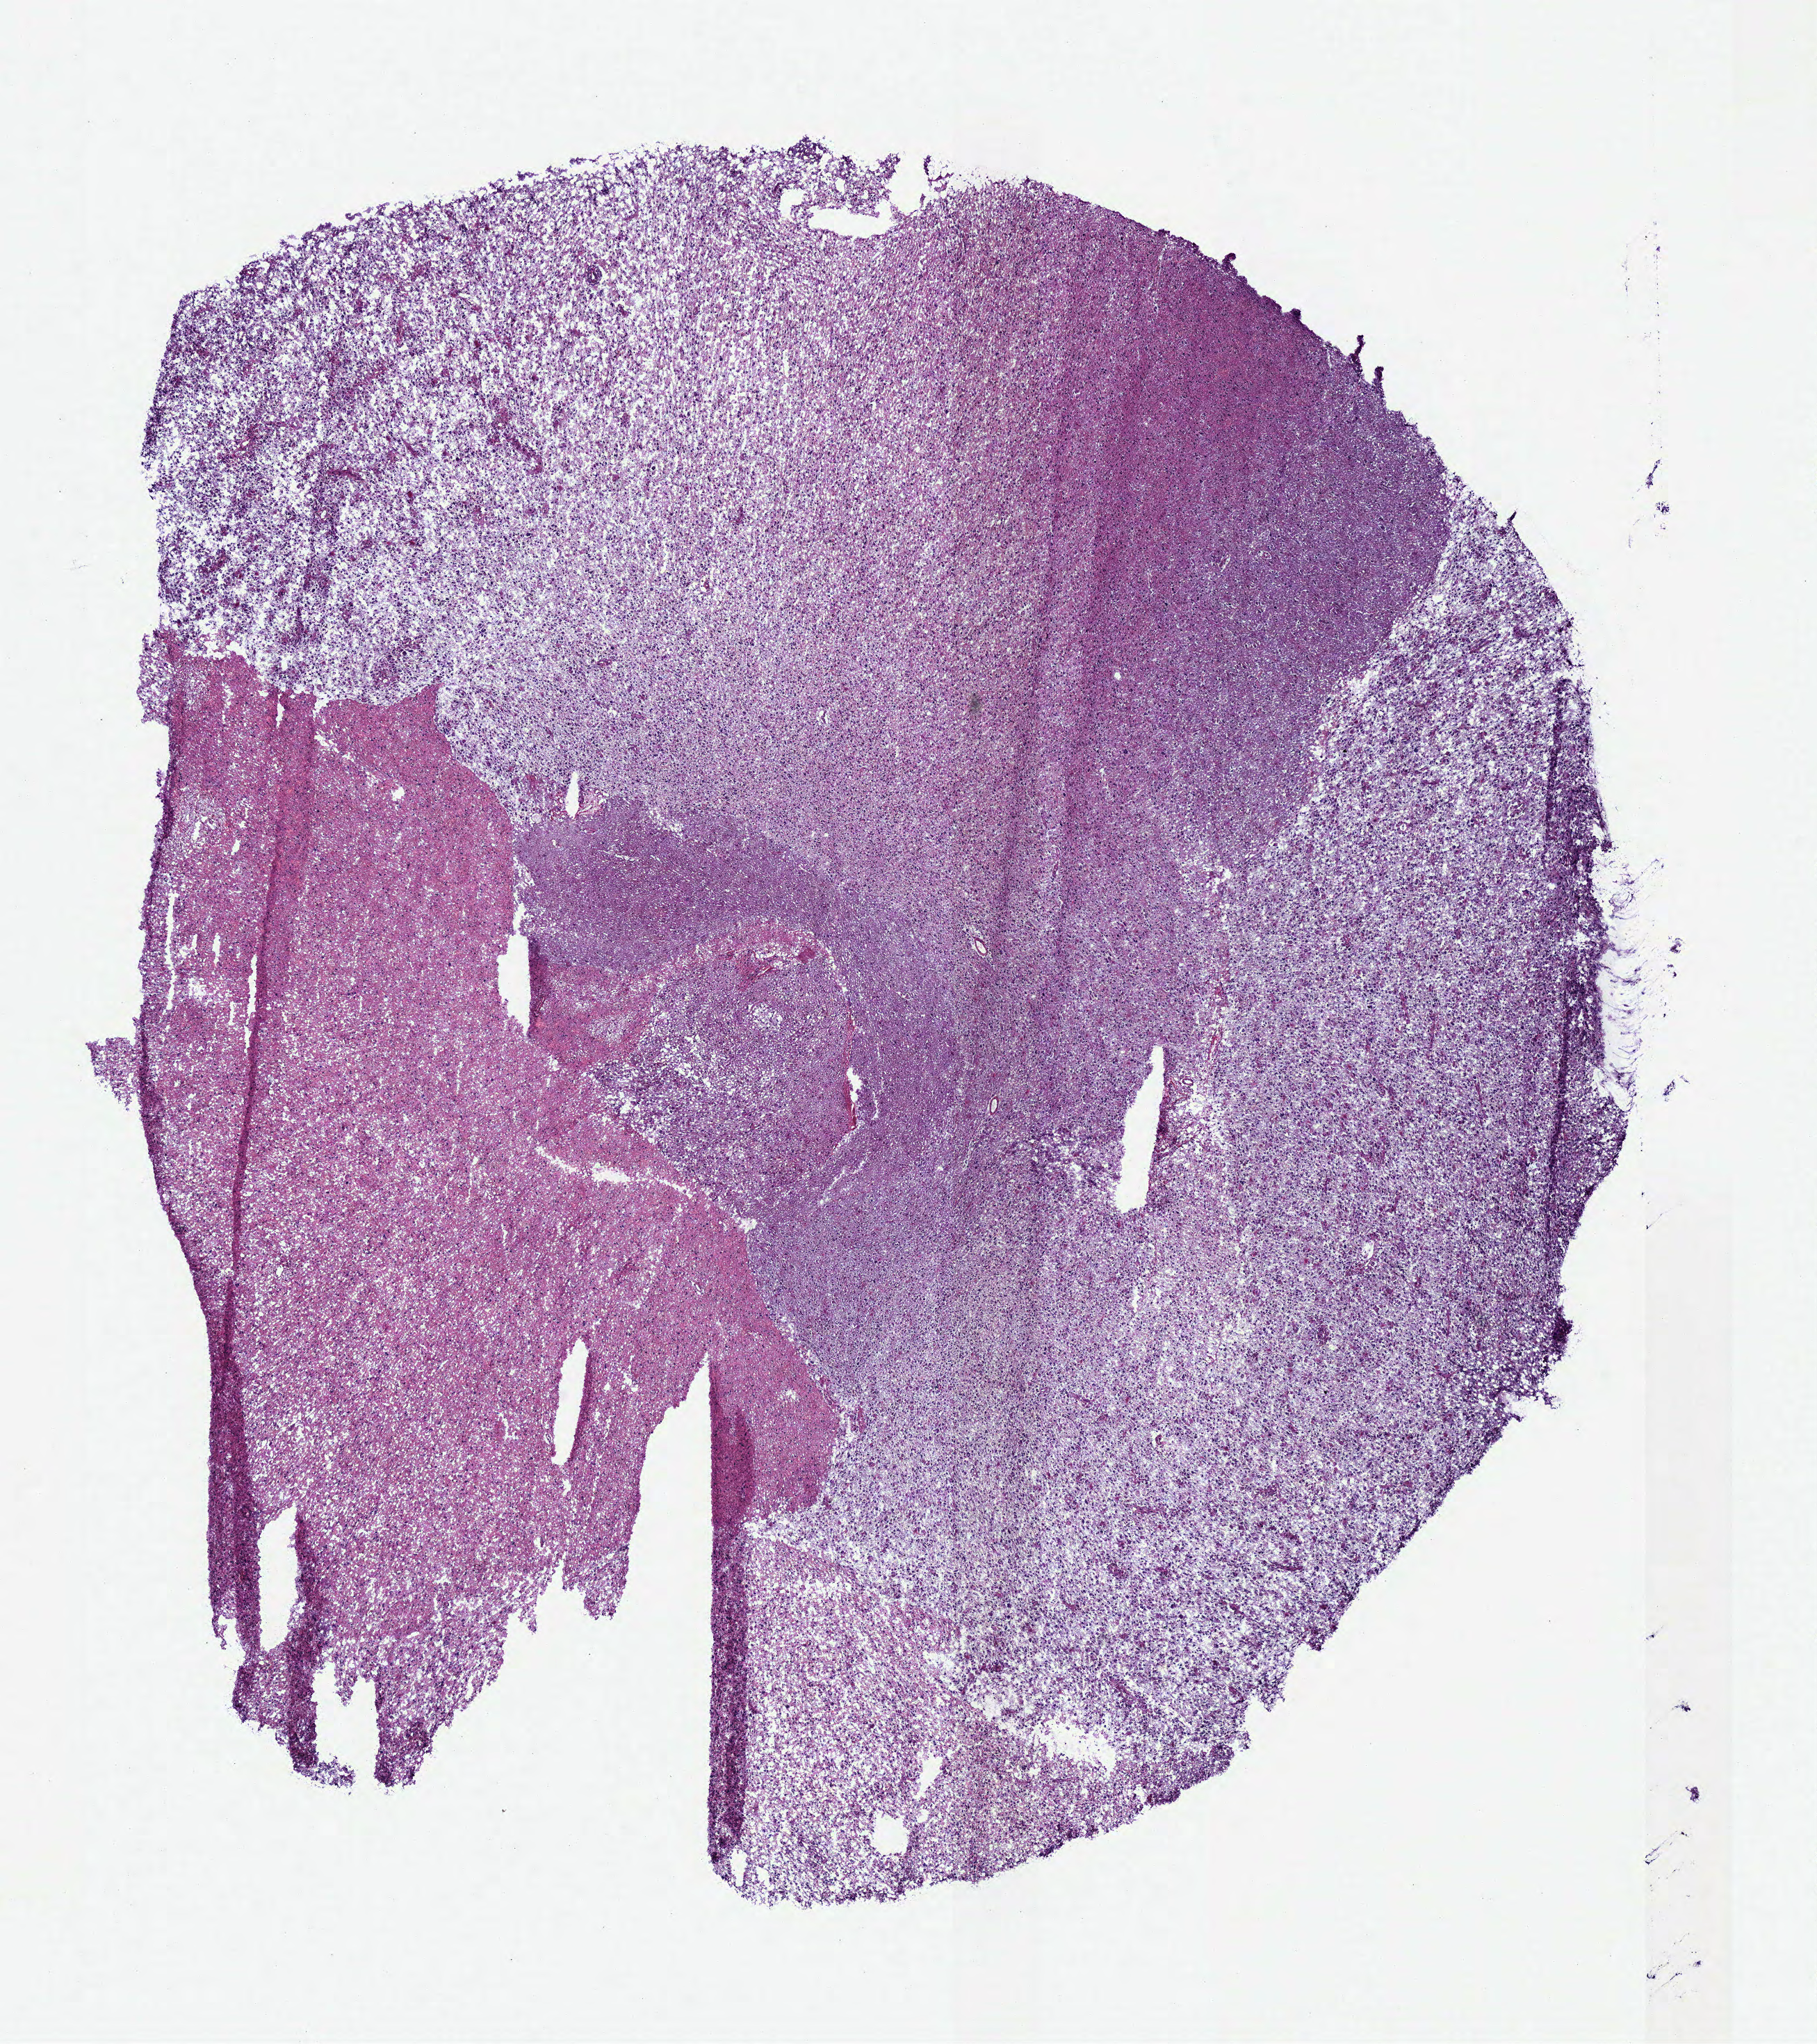
H&E-stained whole-slide image, whole scanned area (about 10.3 x 11.6 mm, from a 40x scan) shown as a low-resolution overview; frozen section from the top of the tissue portion; primary tumour sample from the brain. Female, age 58 years at initial diagnosis. Histologic grade: G3 (poorly differentiated). Composition of this section per pathologist review: tumour cells 100%, tumour nuclei 80%, normal cells 0%, stromal cells 0%, necrosis 0%.
Laterality: left. Pathologic diagnosis: Astrocytoma, anaplastic (cerebrum).